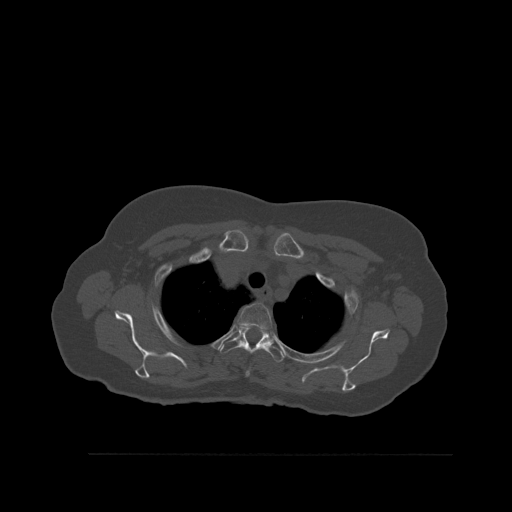
CT including the spine, one axial slice; slice 425 of 527 in the series (ordered by position); bone window (W 1800 / L 400 HU); 512 × 512 image matrix. Patient: female, 73 years. Case-level facts recorded for this patient, not image findings: primary cancer: breast; vertebrae with lytic lesions (as recorded): L2.
Annotated regions visible in this slice (semi-automatic segmentation, software-assisted and operator-edited):
- T2 vertebra: bounding box [x1, y1, x2, y2] px = [237, 303, 272, 376]
- T3 vertebra: [219, 326, 285, 362]